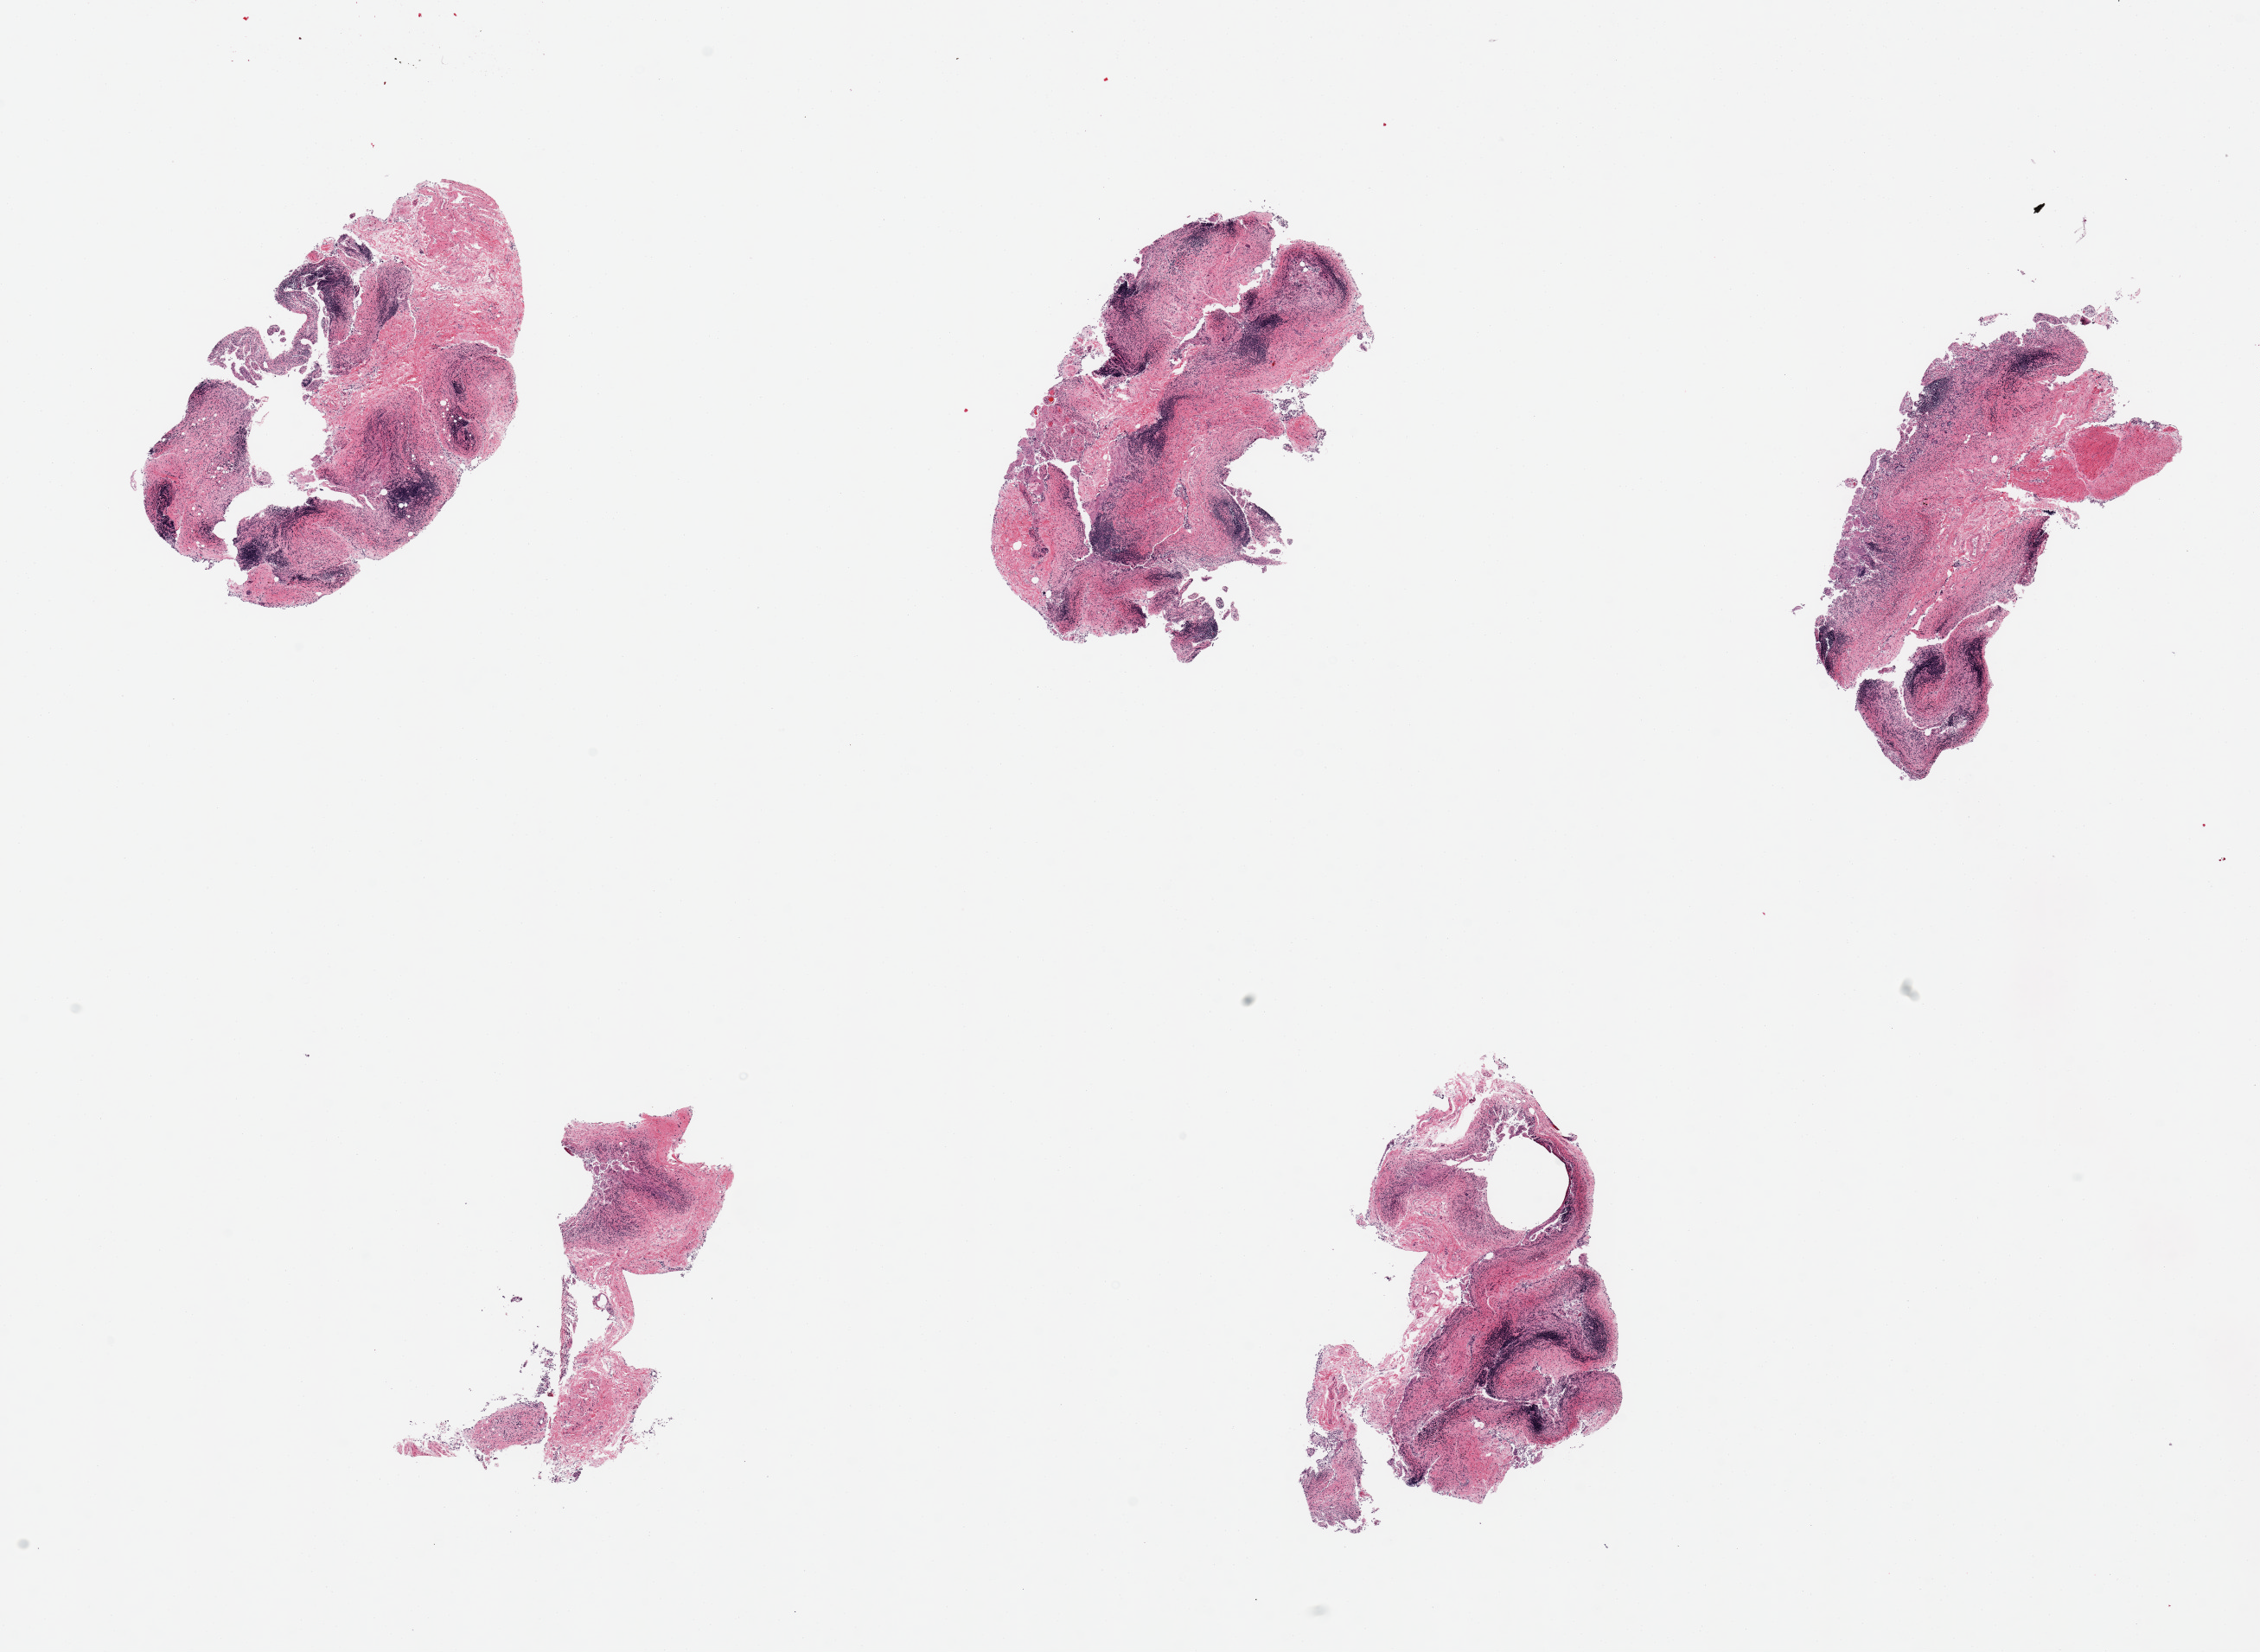
Haematoxylin and eosin whole-slide image — low-resolution overview of the scanned area, about 20.7 x 15.1 mm, PAXgene-fixed paraffin-embedded (PFPE) section, section of ileum (target tissue), tissue donor sample.
Review note (as recorded): 5 pieces; autolyzed mucosa with scattered residual lymphoid aggregates, small focus of muscularis (not target).